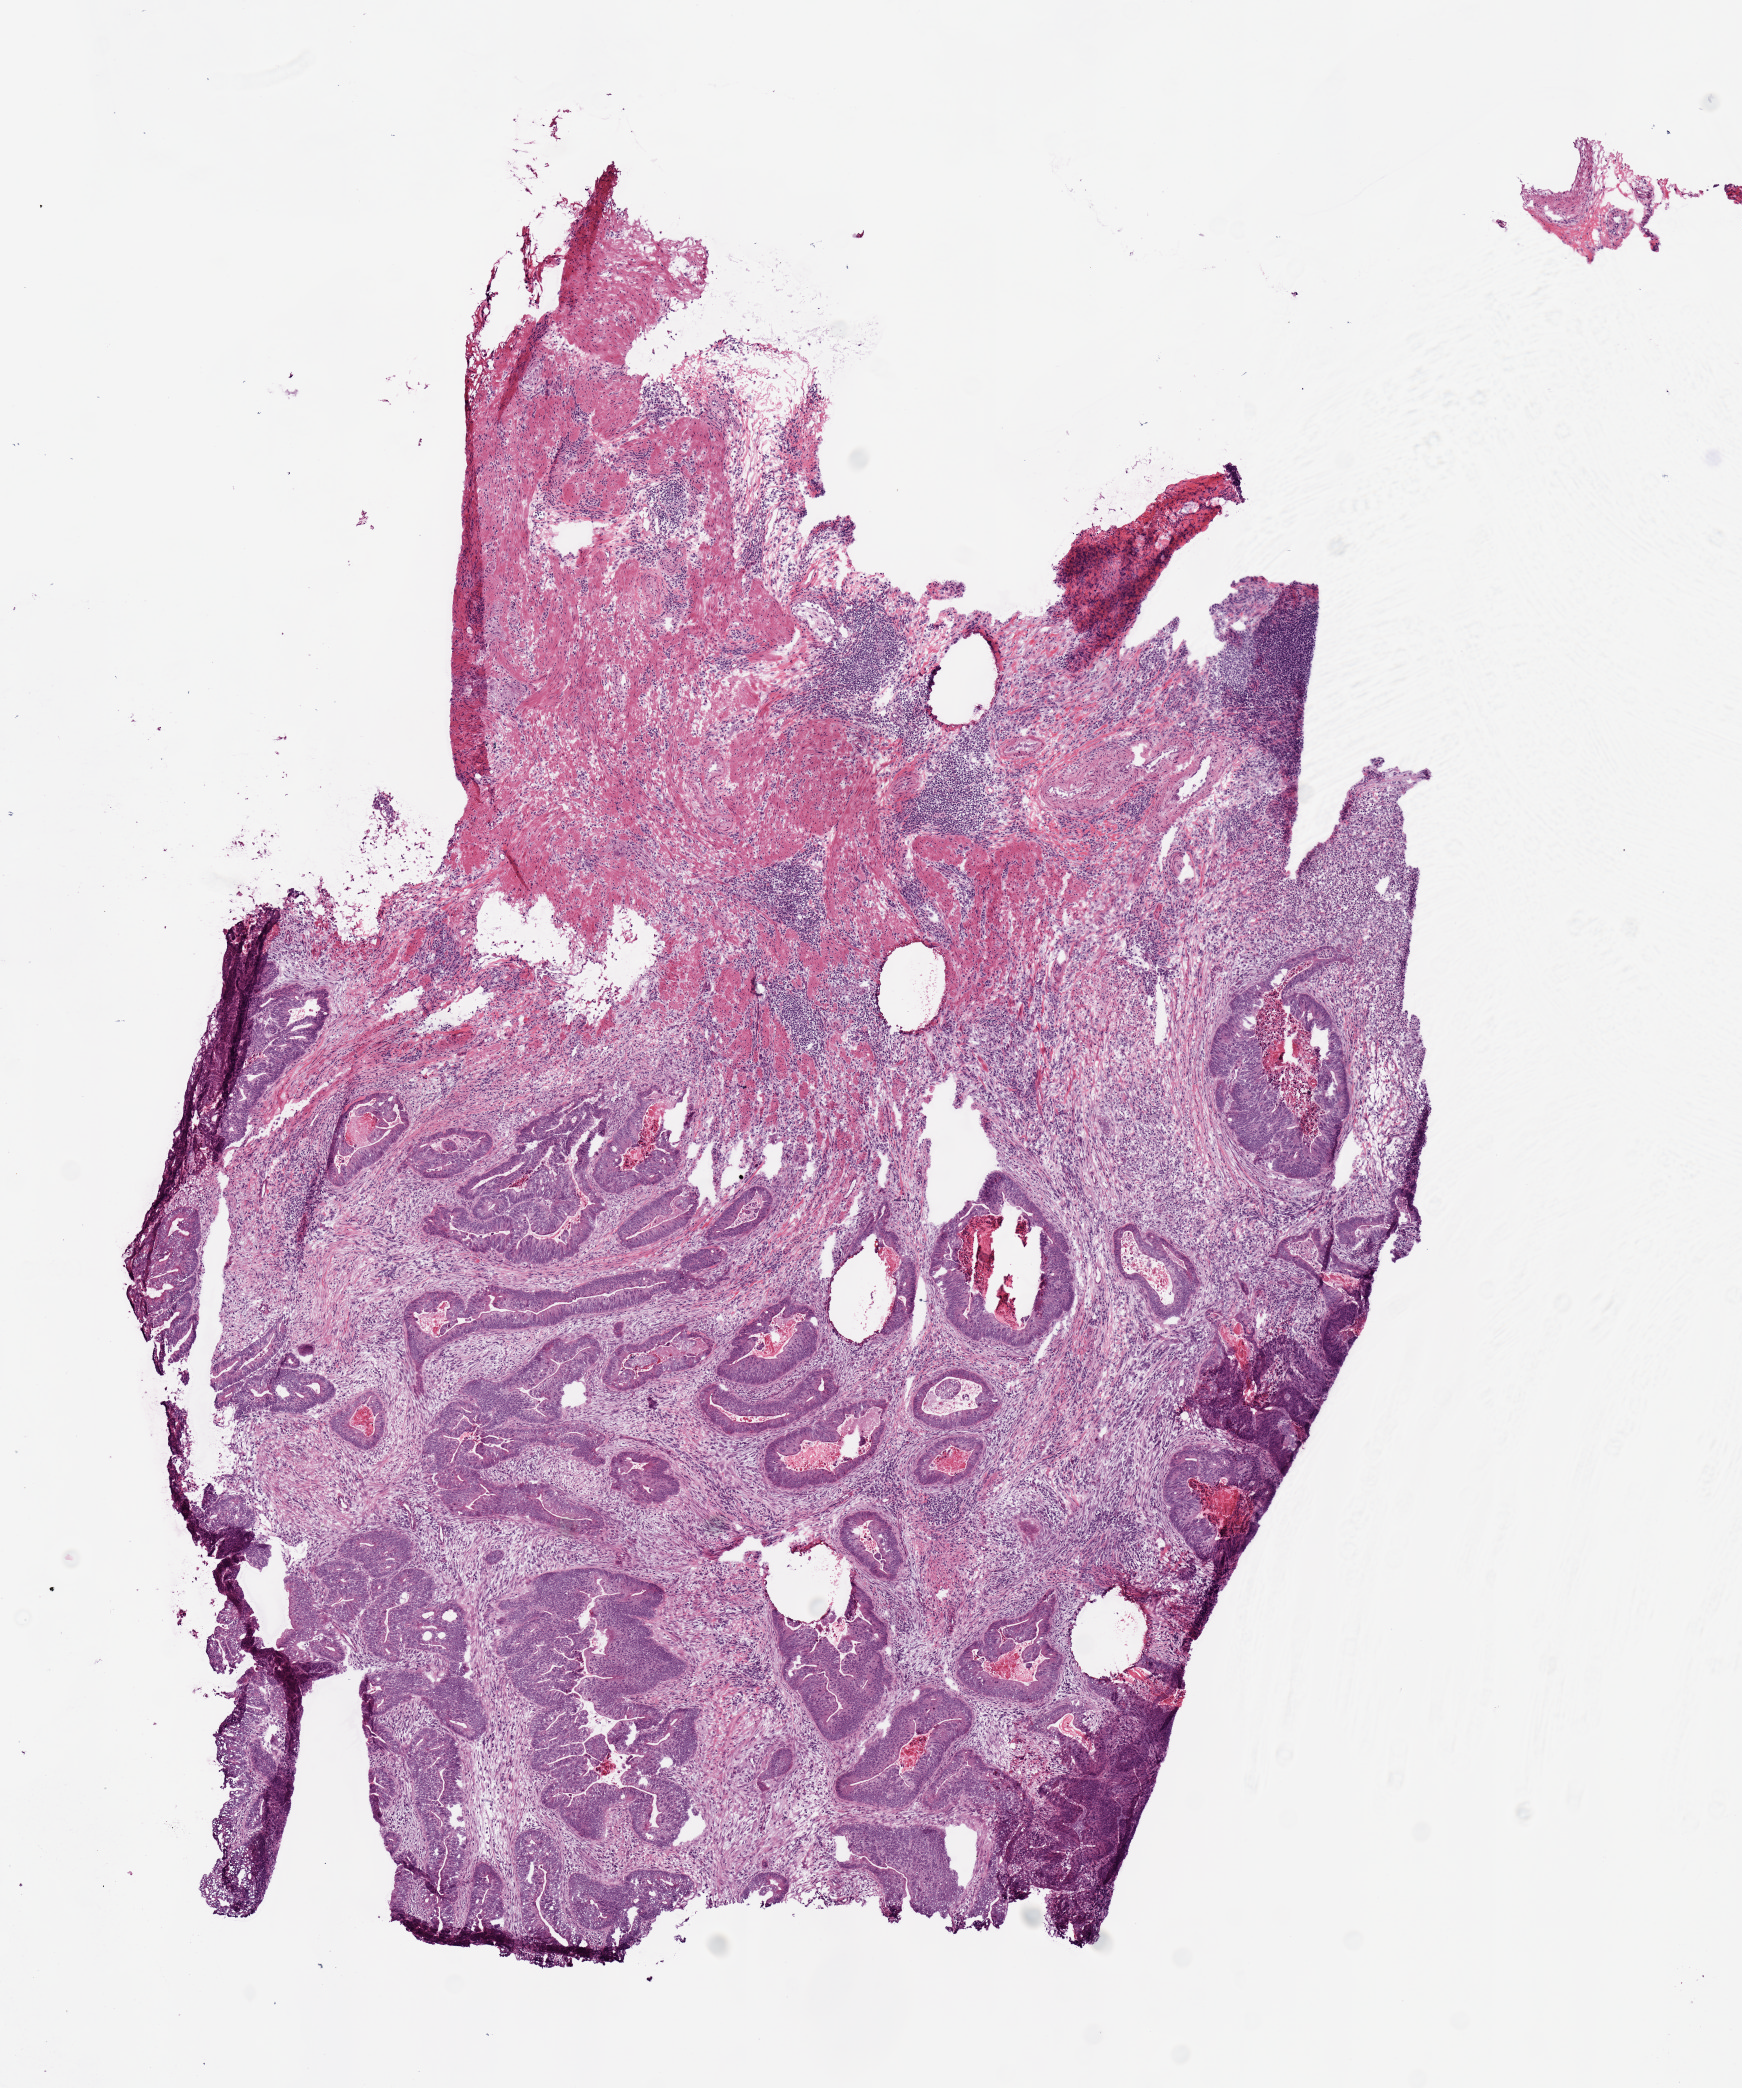
H&E-stained whole-slide image, a low-resolution overview of the entire scanned area, about 6.9 x 8.3 mm (from a 20x scan). Frozen section. Sample: primary tumour, colon. Male patient; age at initial diagnosis 83 years. Pathologist review of this section (percent, as recorded): tumour nuclei 65%, normal cells 0%, stromal cells 15%, necrosis 18%.
Lymph nodes positive (case pathology): 7 of 10 examined. Histologic diagnosis: Adenocarcinoma, NOS.